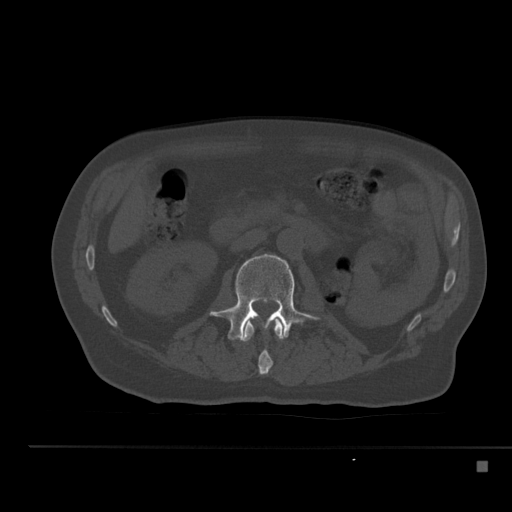
CT including the spine, one axial slice. Slice 190 of 517 in the series (ordered by position). 120 kVp. Bone window (W 1800 / L 400 HU). 1.5 mm slice thickness. 512 × 512 image matrix, field of view 408 × 408 mm. Male patient, age 70 years. From the clinical record (not read from this slice): primary cancer: renal; vertebrae with lytic lesions (as recorded): T4, T6, T10, T12, L3, L4, L5.
Structures marked on this image (semi-automatic segmentation, software-assisted and operator-edited):
- L1 vertebra: box from (x=240, y=318) to (x=286, y=375) px
- L2 vertebra: (x=210, y=254)–(x=321, y=340)